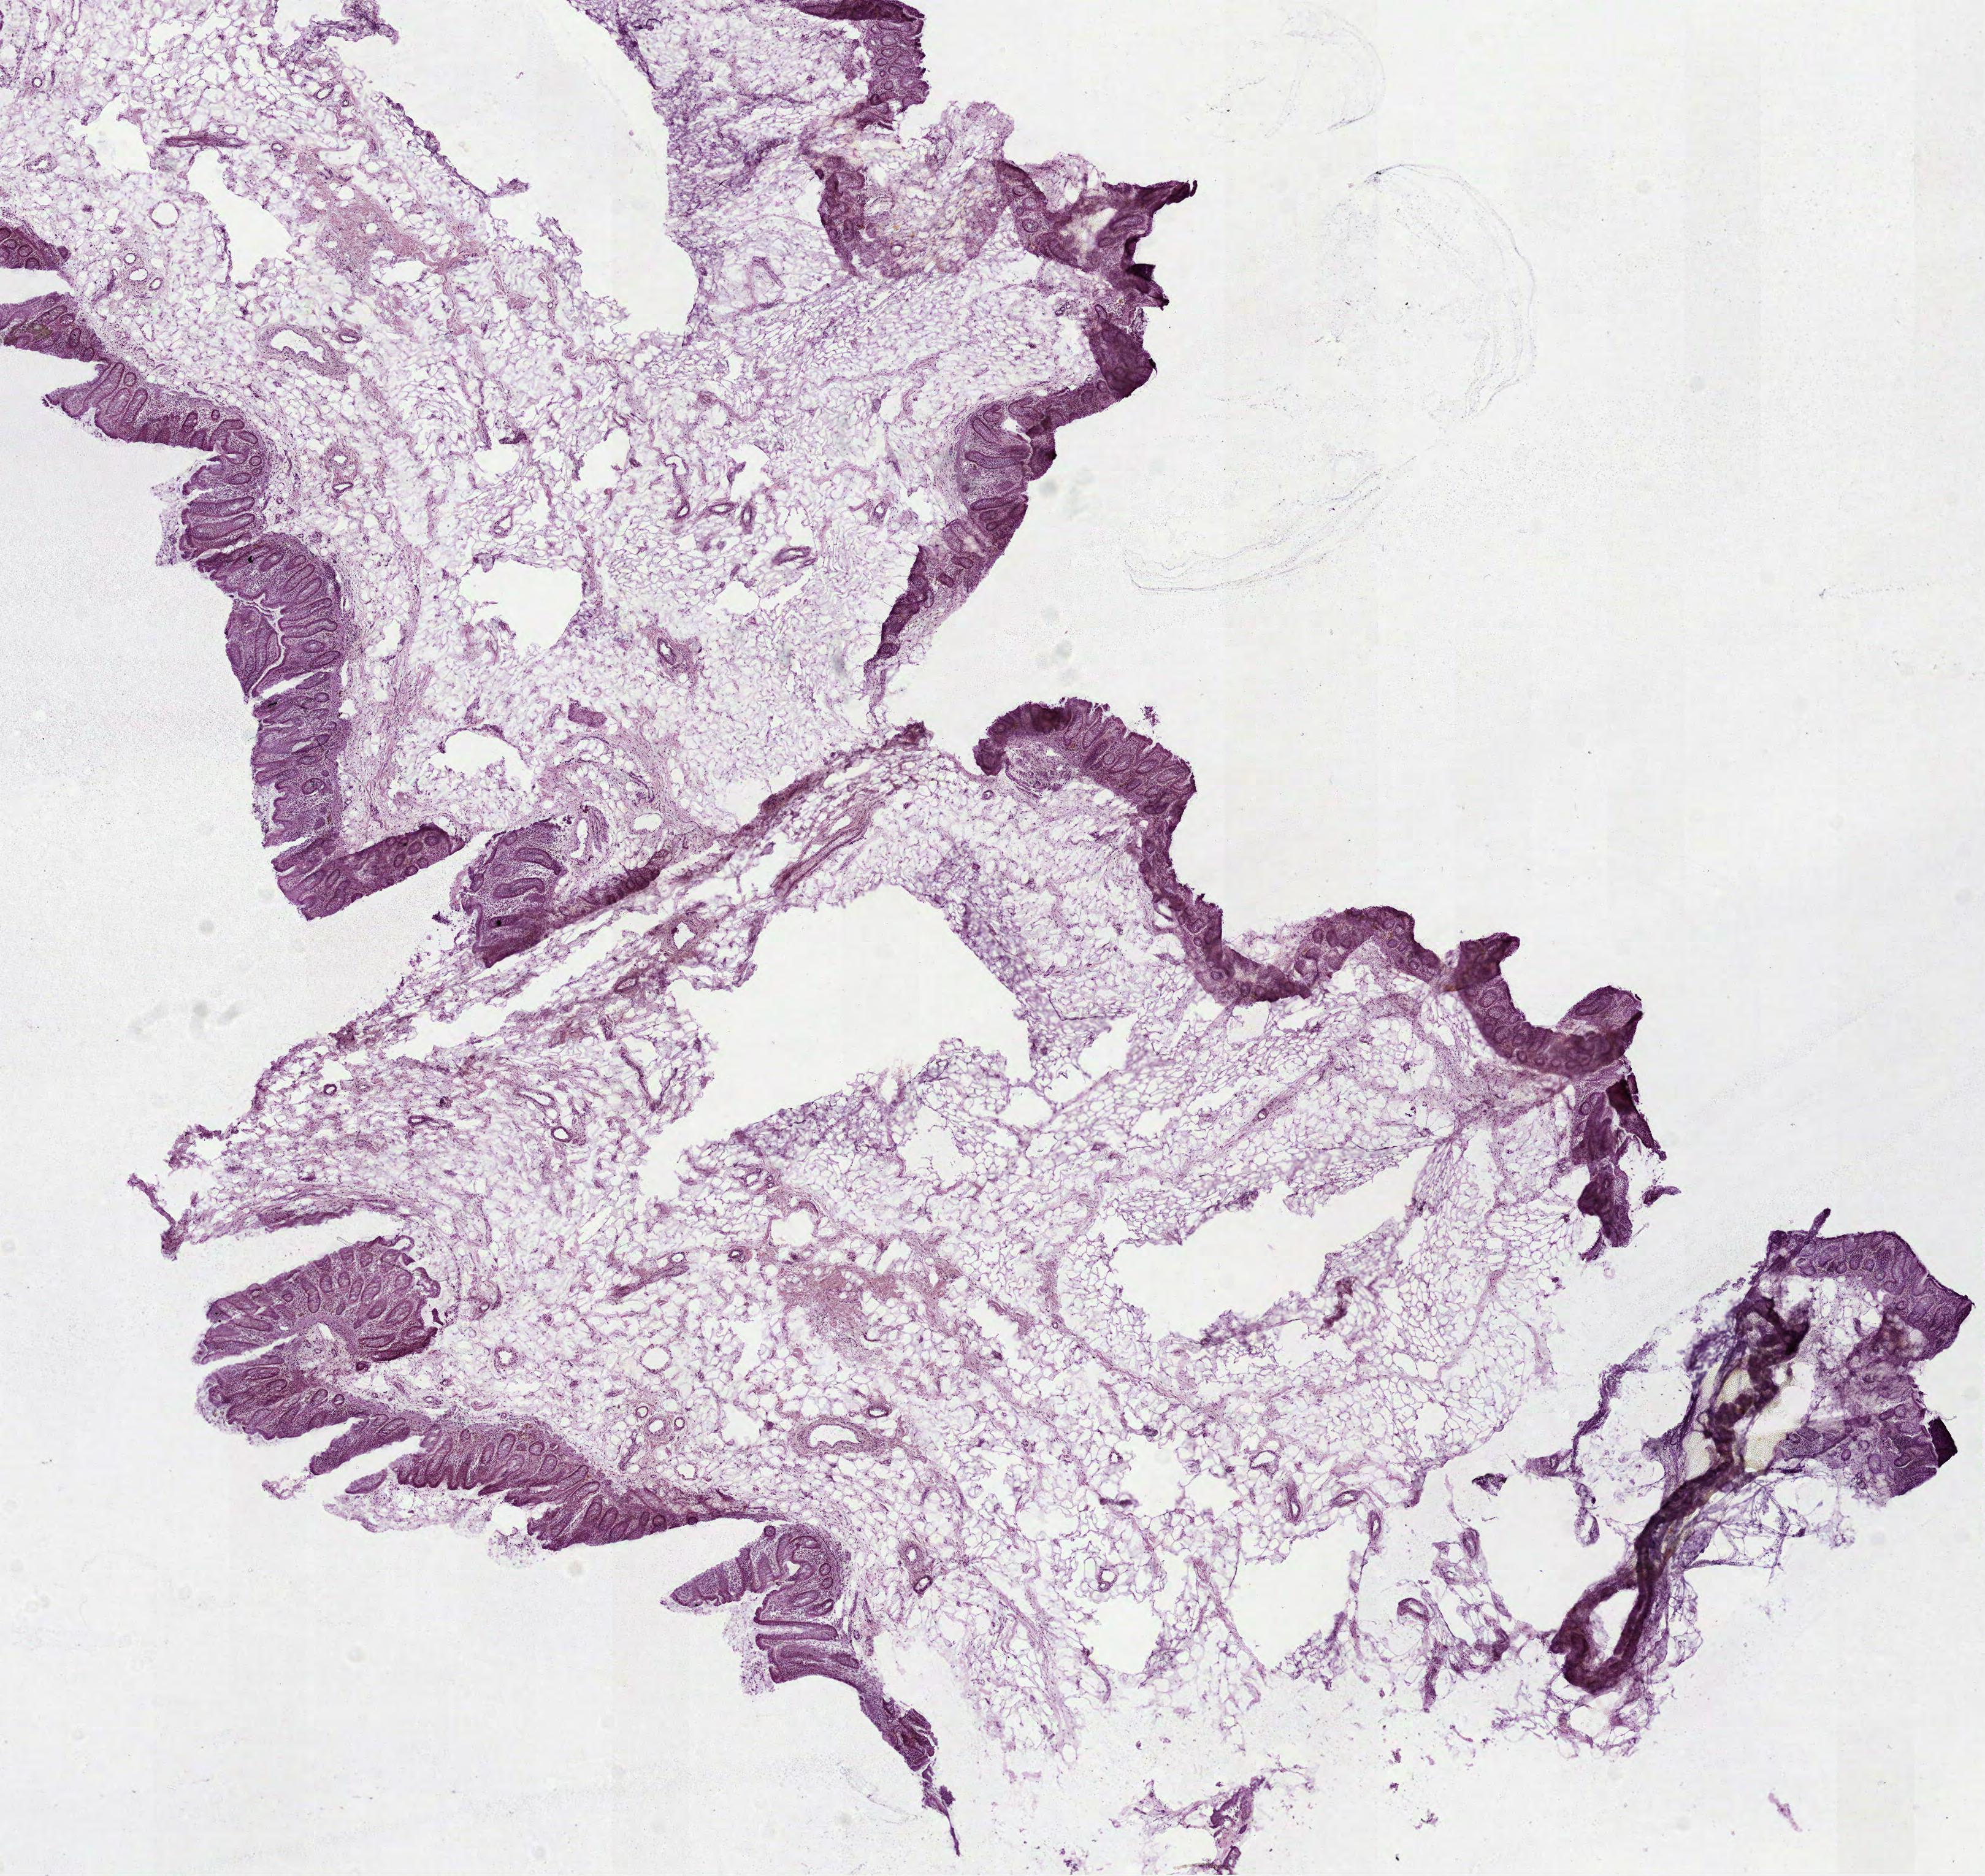
Whole-slide histology image, H&E, low-resolution overview of the scanned area, about 13.1 x 12.3 mm (slide scanned at 40x); frozen section from the top of the tissue portion; solid tissue normal (non-tumour tissue) sample from the colon. Female patient; age at initial diagnosis 70 years.
This section: solid tissue normal sample (biorepository sample class). Patient diagnosis: Adenocarcinoma, NOS (cecum).